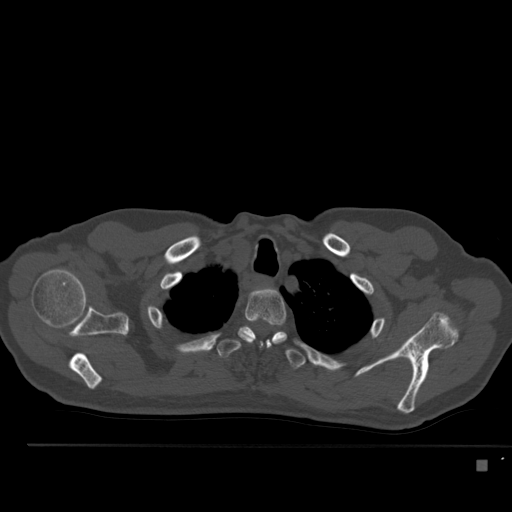
CT including the spine, one axial slice. Position 407 of 517 along the scan axis. Reconstruction kernel Br40s. 120 kVp. Bone window (W 1800 / L 400 HU). 512 × 512 image matrix. Male patient, age 70 years. Case-level facts recorded for this patient, not image findings: primary cancer: renal.
Outlined on this slice (semi-automatic segmentation, software-assisted and operator-edited):
- T2 vertebra: bounding box [x1, y1, x2, y2] px = [238, 289, 287, 346]
- T3 vertebra: [216, 326, 308, 369]